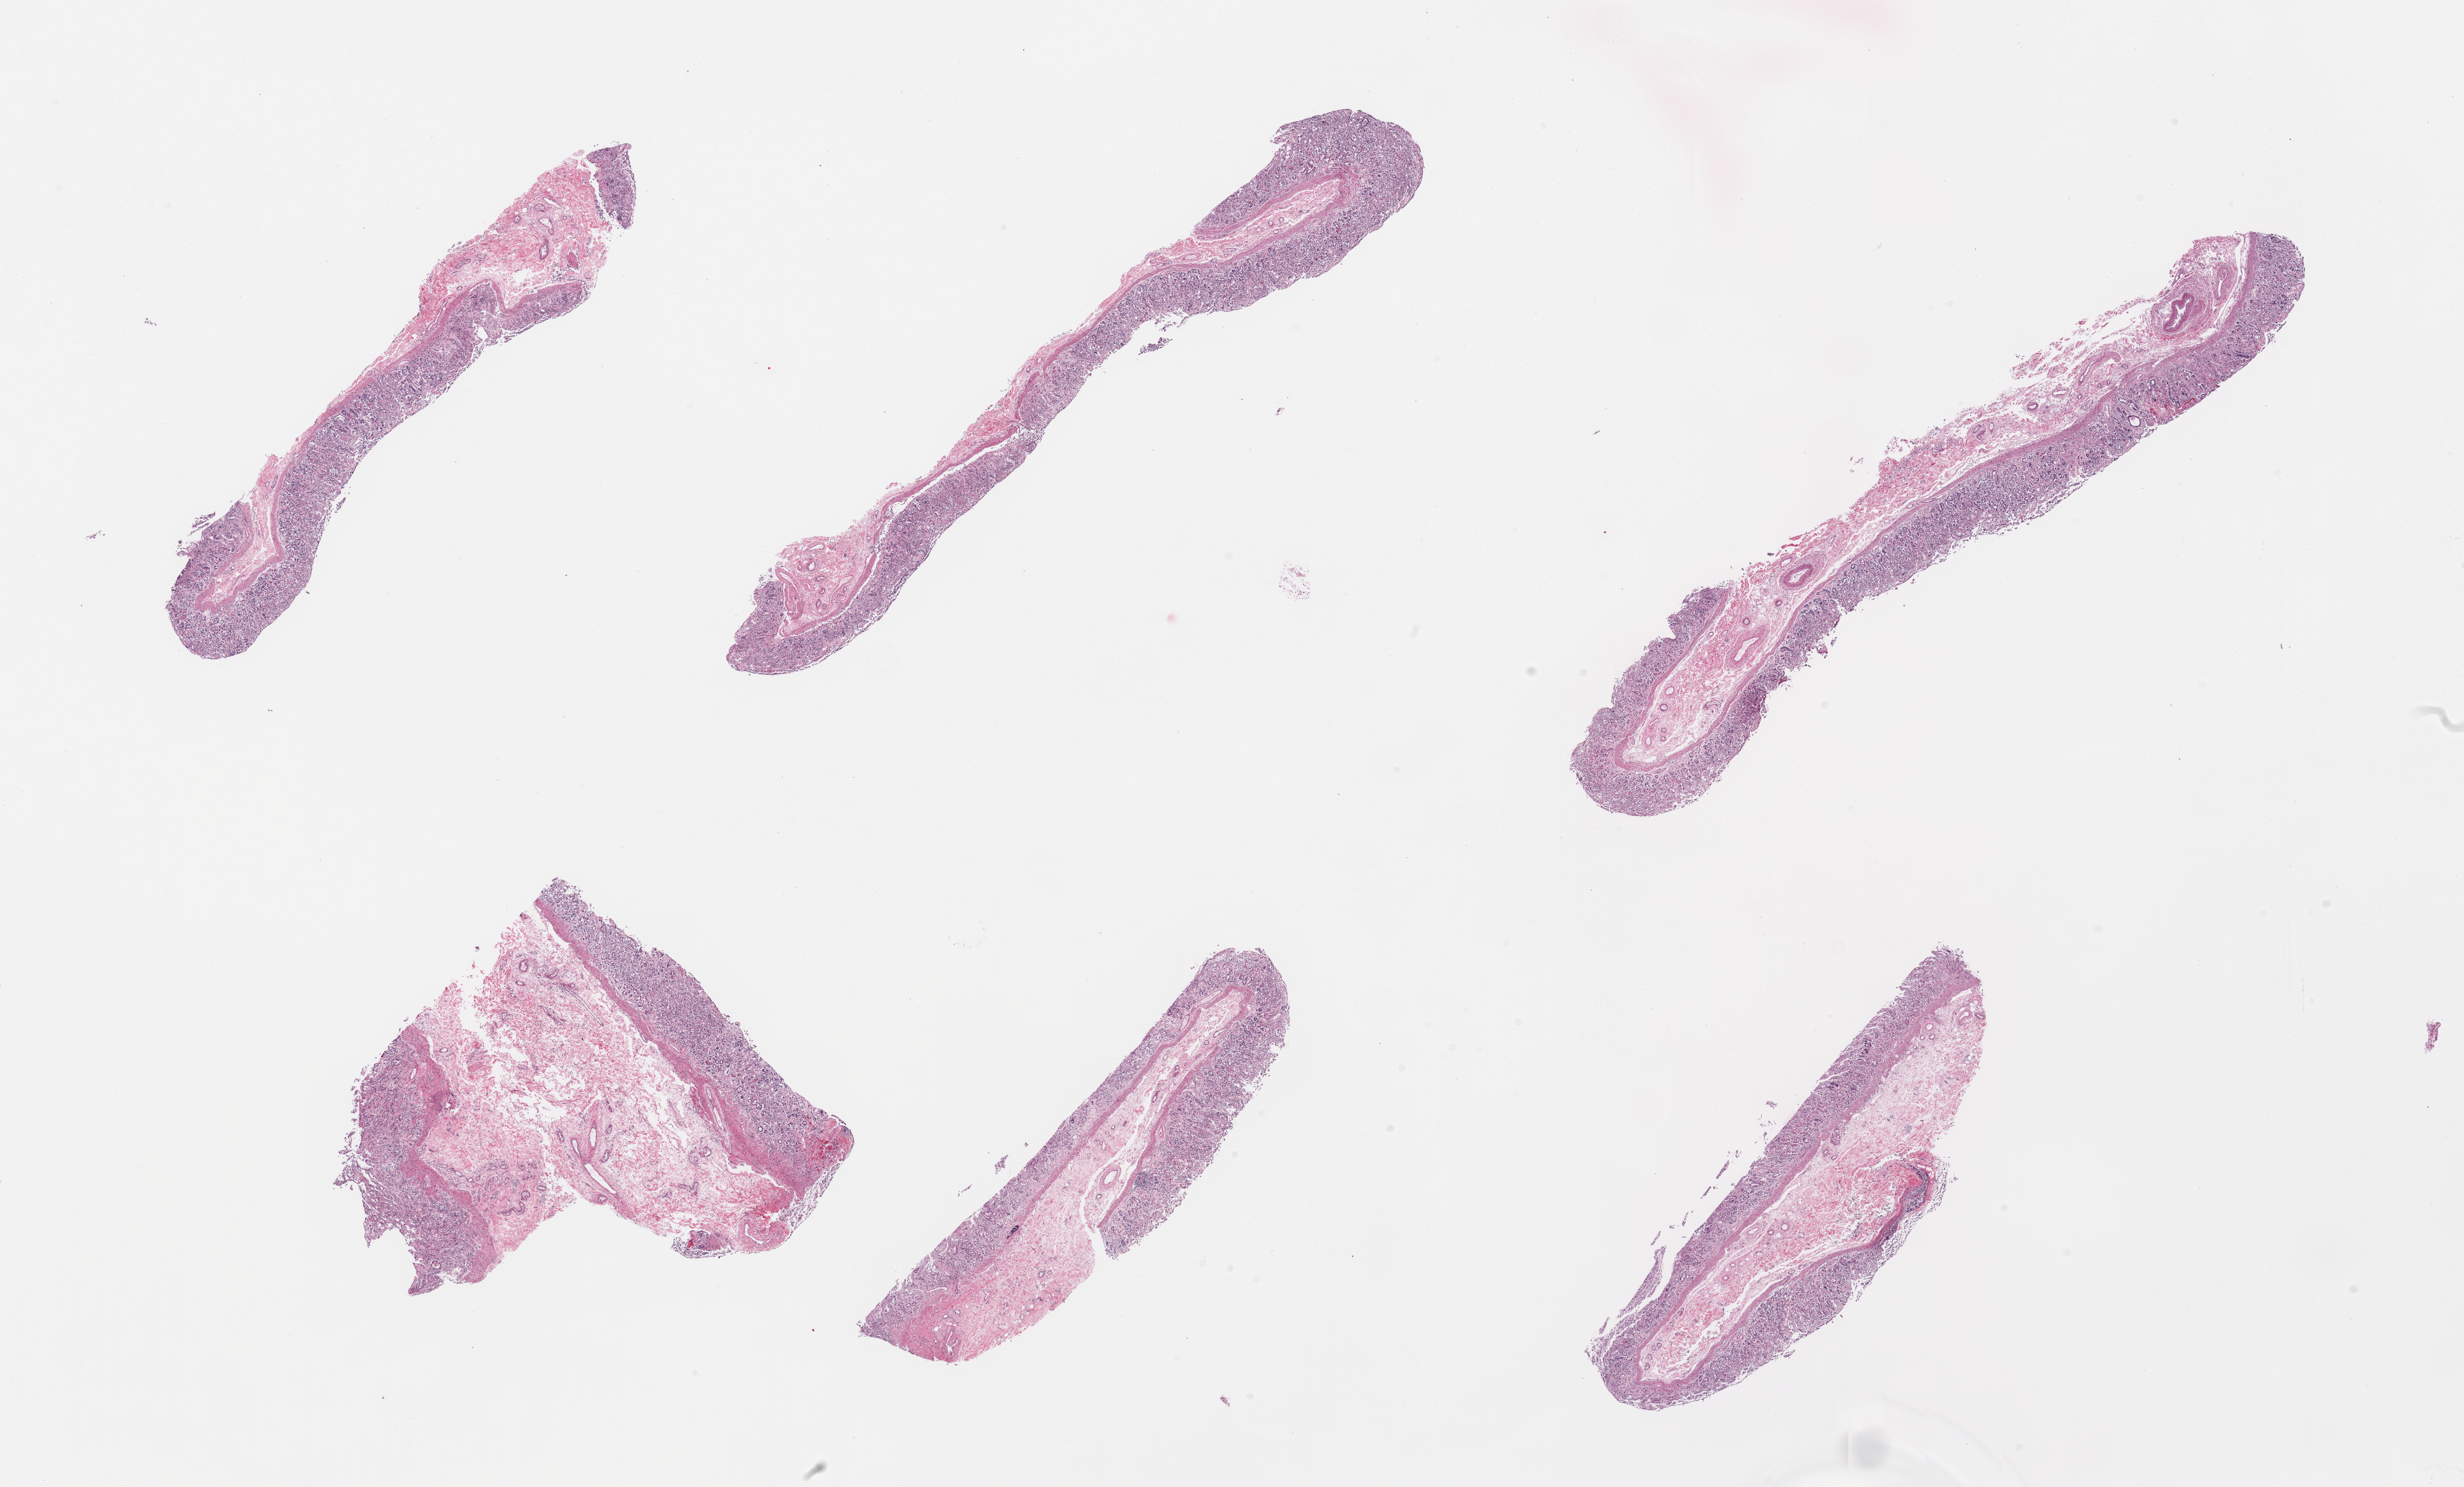
Whole-slide image, hematoxylin and eosin (H&E) stain — low-resolution overview of the scanned area, about 31.5 x 19.0 mm; PAXgene-fixed paraffin-embedded (PFPE) section; target tissue: stomach; tissue donor sample. Male donor.
Reviewer comment on this tissue sample: 6 pieces, mucosa is up to ~0.6mm, 40-80% thickness, markedly autolyzed.